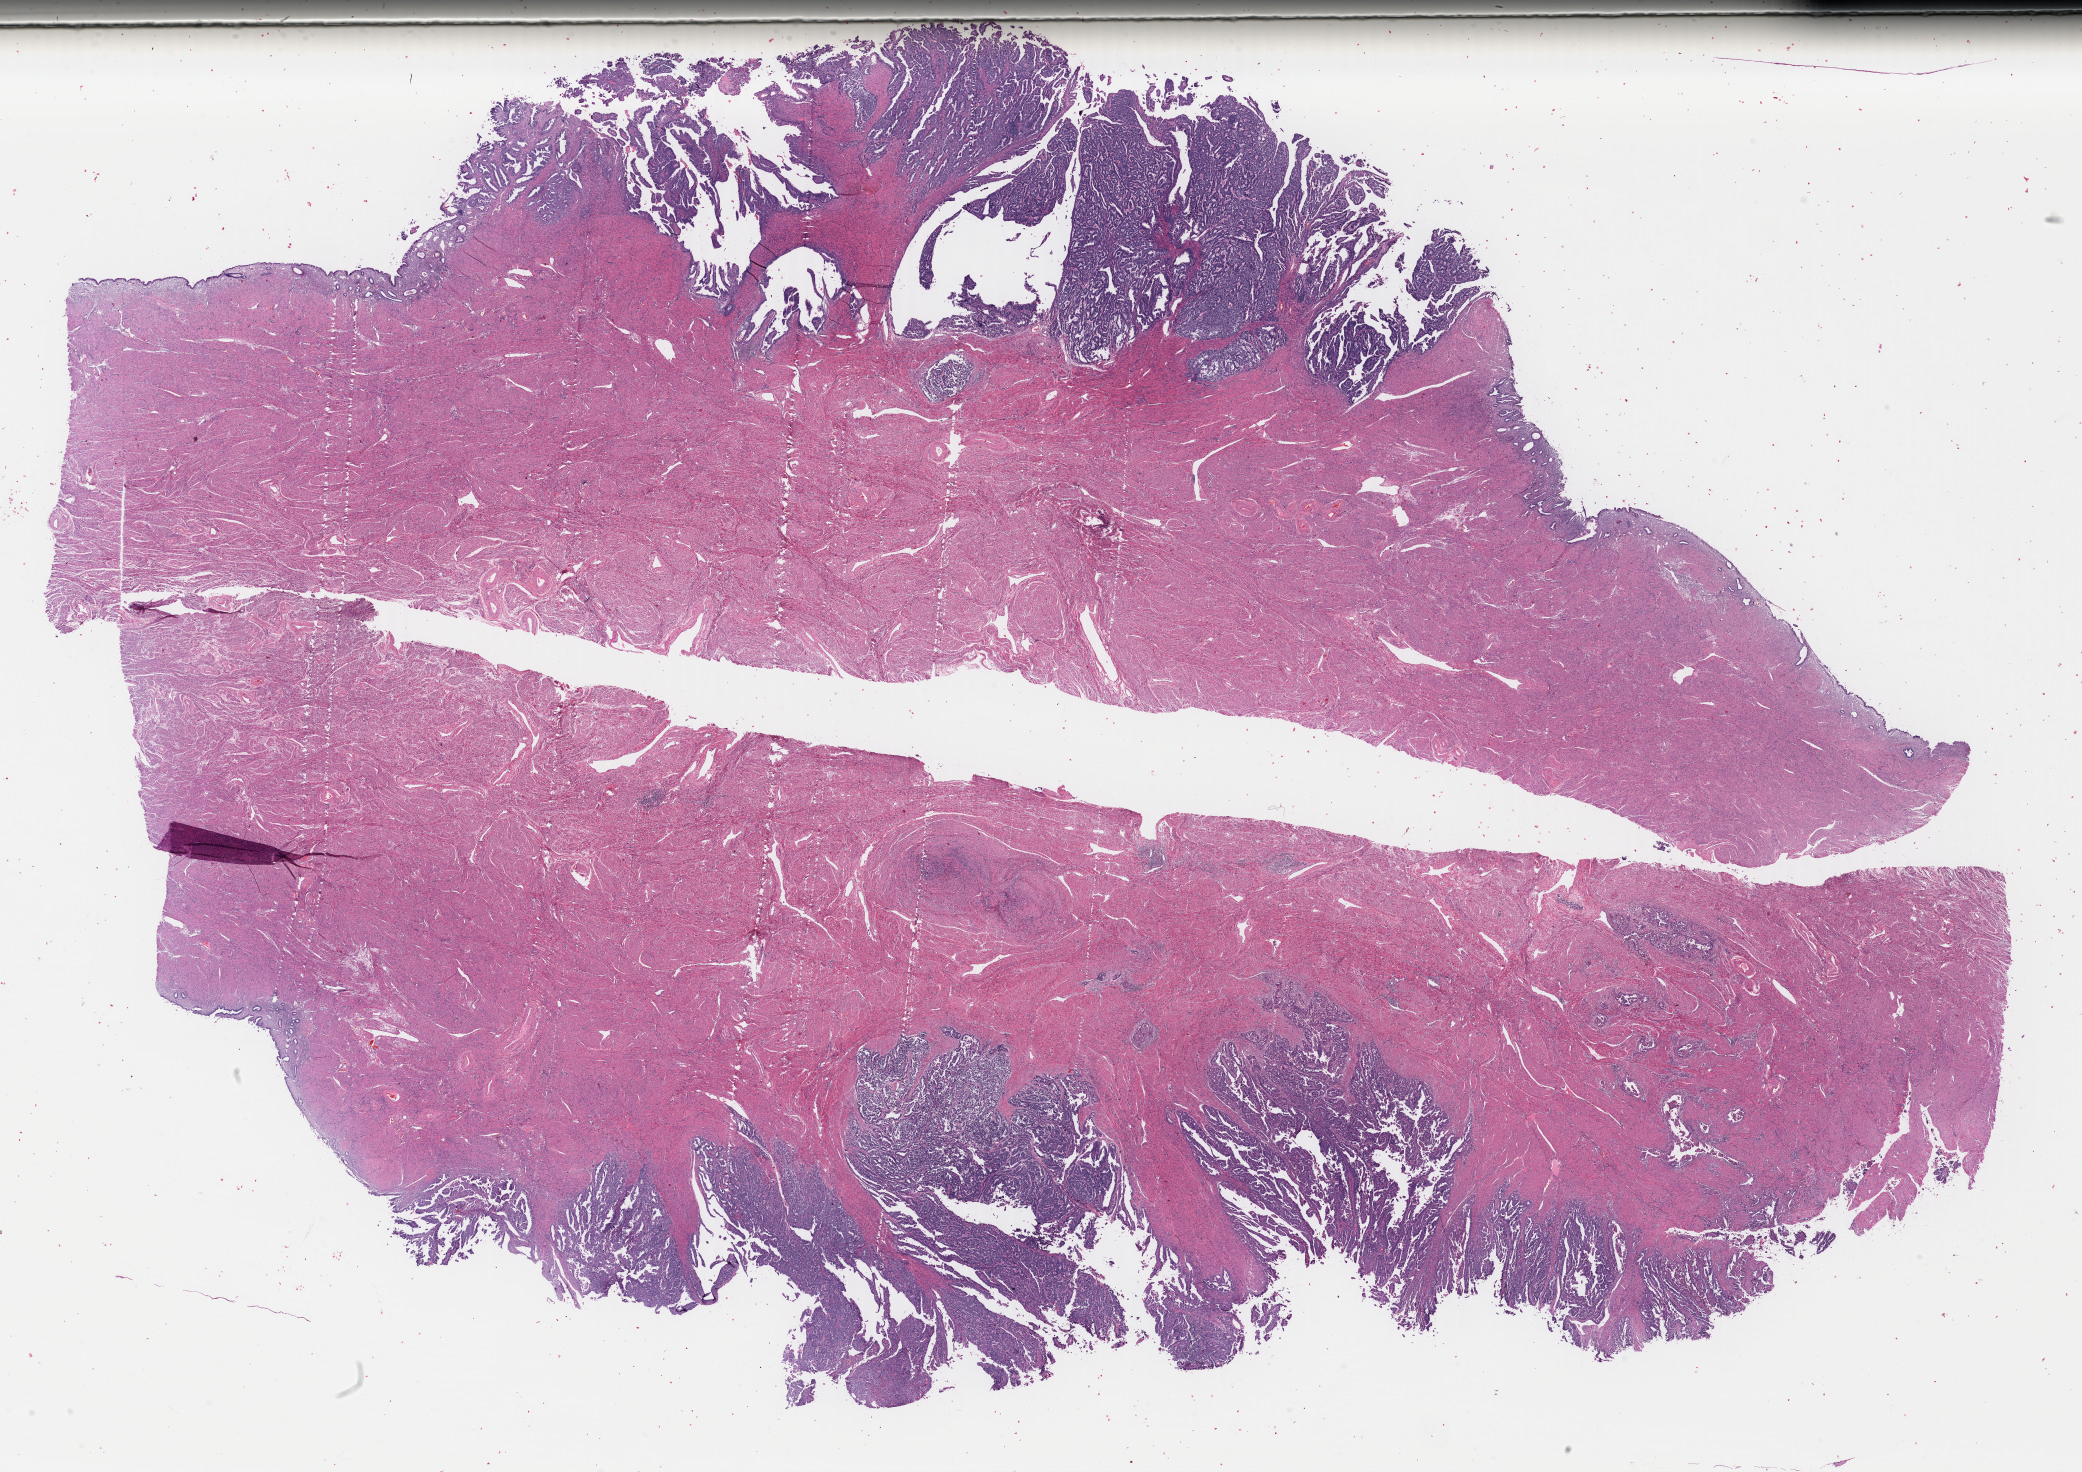
H&E whole-slide image — whole scanned area (about 32.7 x 23.1 mm) shown as a low-resolution overview. Formalin-fixed paraffin-embedded (FFPE) diagnostic section. Uterus, primary tumour sample. Female, age 60 years at initial diagnosis. Histologic grade: G3 (poorly differentiated).
Lymph nodes positive (case pathology): 0 of 4 examined. FIGO stage: IC. Histologic diagnosis: Serous cystadenocarcinoma, NOS (endometrium).